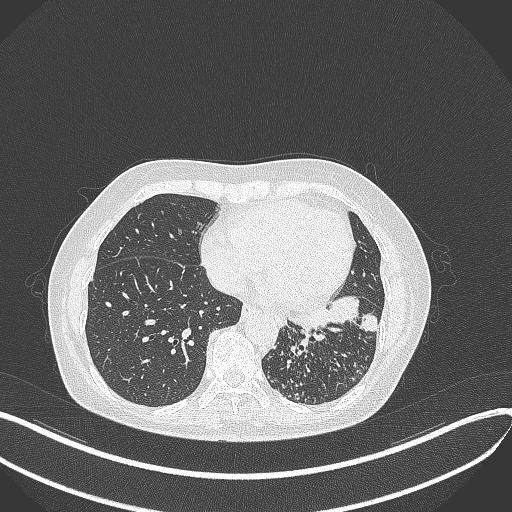
Chest CT, one axial slice. Position 141 of 429 along the scan axis. 100 kVp. Lung window (W 1500 / L -600 HU). 512 × 512 image matrix, field of view 400 × 400 mm. Patient: female, 63 years. Case-level facts recorded for this patient, not image findings: clinical TNM (as recorded): T1b N0 M0.
Outlined on this slice (rectangle marked by the reading radiologist):
- lung tumour (recorded histology: adenocarcinoma): bounding box <287,293,382,338> (left, top, right, bottom; pixels)